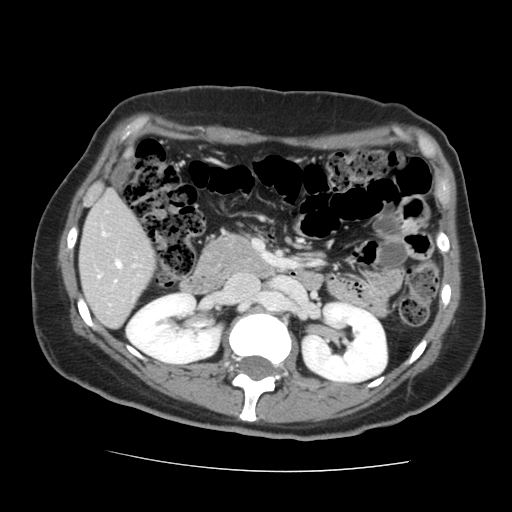
Contrast-enhanced abdominal CT, one axial slice; position 67 of 144 along the scan axis; 120 kVp; soft-tissue window (W 400 / L 40 HU); 2.5 mm slice thickness; 512 × 512 image matrix, field of view 333 × 333 mm. Female patient, age 46 years. Case-level facts recorded for this patient, not image findings: diagnosis: colorectal cancer liver metastases, imaged before liver resection; multiple liver metastases: no; largest metastasis: 2.8 cm.
Structures marked on this image (expert manual segmentation):
- liver: bounding box [x1, y1, x2, y2] px = [80, 193, 154, 327]
- planned liver remnant (the part of the liver to remain after resection): [80, 193, 154, 324]
- portal vein (with intrahepatic branches): [98, 233, 121, 283]